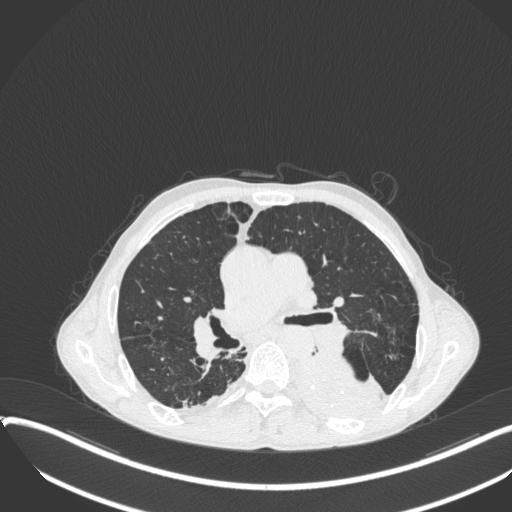
Chest CT, one axial slice; slice 220 of 400 in the series (ordered by position); 120 kVp; lung window (W 1500 / L -600 HU); 1 mm slice thickness; 512 × 512 image matrix, field of view 400 × 400 mm. Patient: male, 57 years. Case-level facts recorded for this patient, not image findings: clinical TNM (as recorded): T4 N0 M0.
Outlined on this slice (bounding box drawn by a radiologist):
- lung tumour (recorded histology: squamous cell carcinoma): bounding box [x1, y1, x2, y2] px = [294, 346, 390, 423]